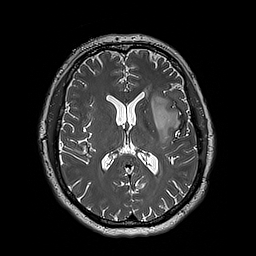
Brain MRI from a brain-tumour surgery series, one axial slice. 1 mm slice thickness. 256 × 256 image matrix, field of view 250 × 250 mm. From the clinical record (not read from this slice): histopathology: Astrocytoma; WHO grade: 3; IDH mutation: yes; tumour location: Left Insular.
Outlined on this slice (manually delineated by an expert):
- tumour: bounding box [x1, y1, x2, y2] px = [151, 95, 182, 145]